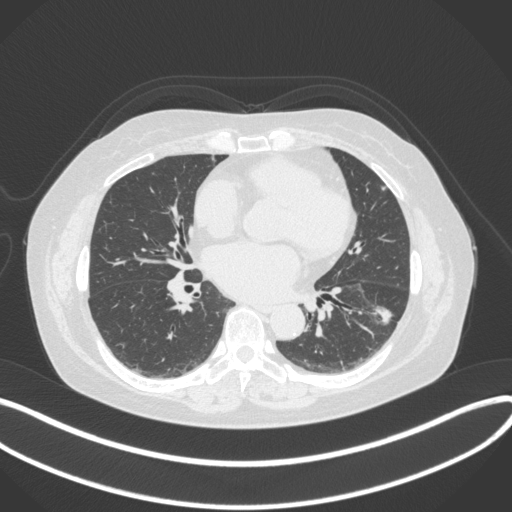
Chest CT, one axial slice; position 166 of 373 along the scan axis; lung window (W 1500 / L -600 HU); 512 × 512 image matrix. Female patient, age 67 years. Case-level facts recorded for this patient, not image findings: clinical TNM (as recorded): T1c N0 M0.
Outlined on this slice (bounding box drawn by a radiologist):
- lung tumour (recorded histology: adenocarcinoma): box from (x=362, y=293) to (x=405, y=331) px